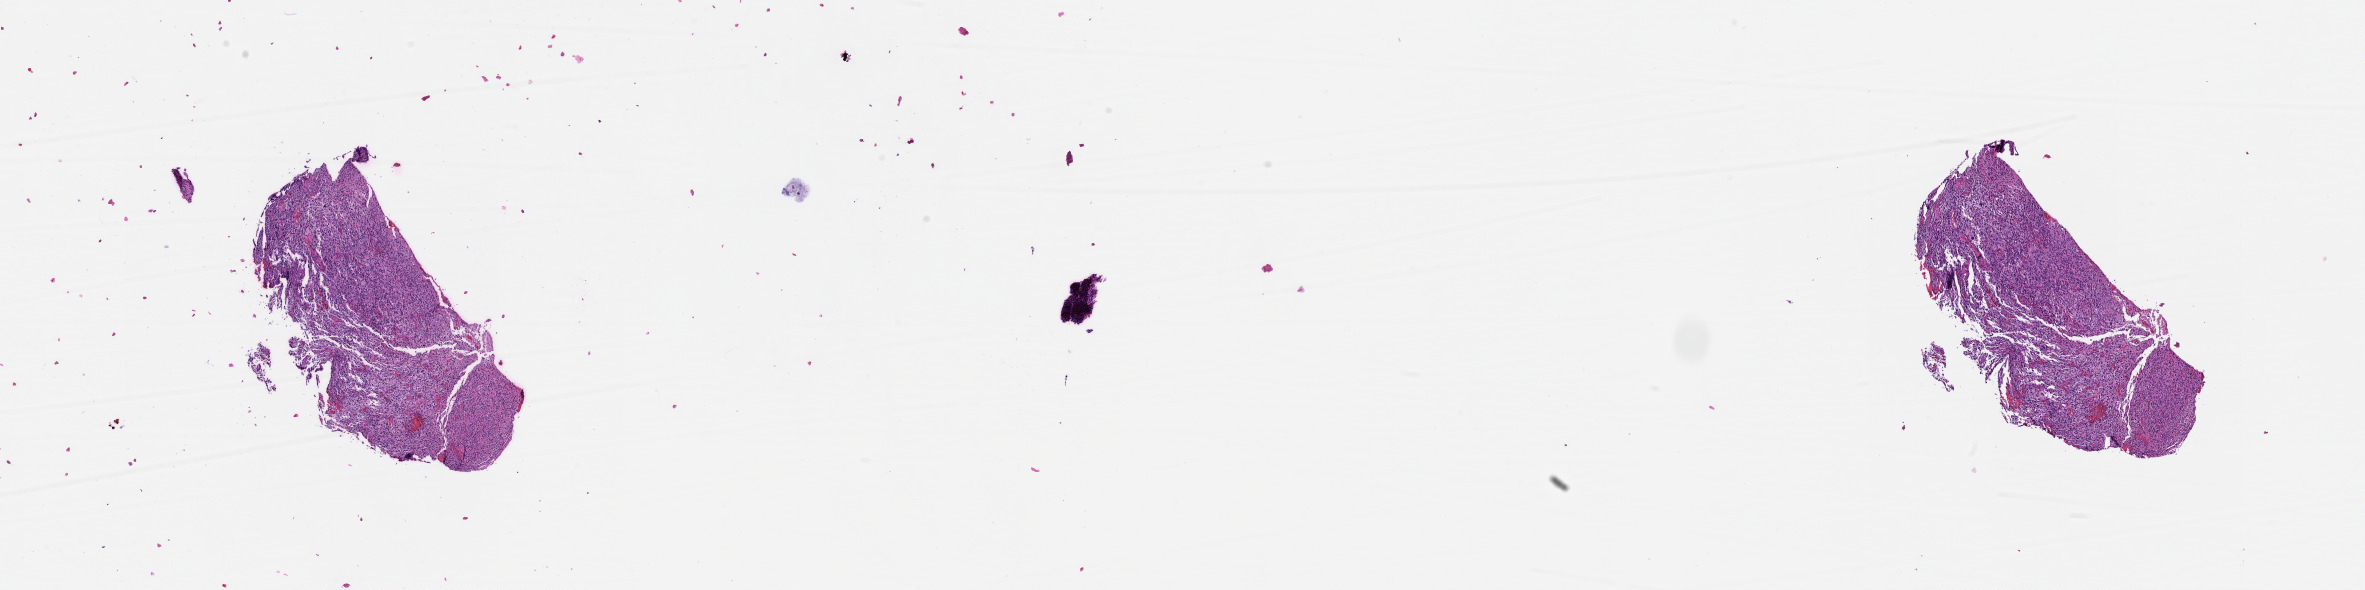
Whole-slide histology image, H&E-stained — a low-resolution overview of the entire scanned area, about 19.0 x 4.8 mm, tumour tissue sample, sampled site: brain. Patient: female, age 71 years. Composition of this section per pathologist review: tumour nuclei 80%, necrosis 5%.
Diagnosis: Glioblastoma. Primary tumour site (as recorded): frontal lobe.